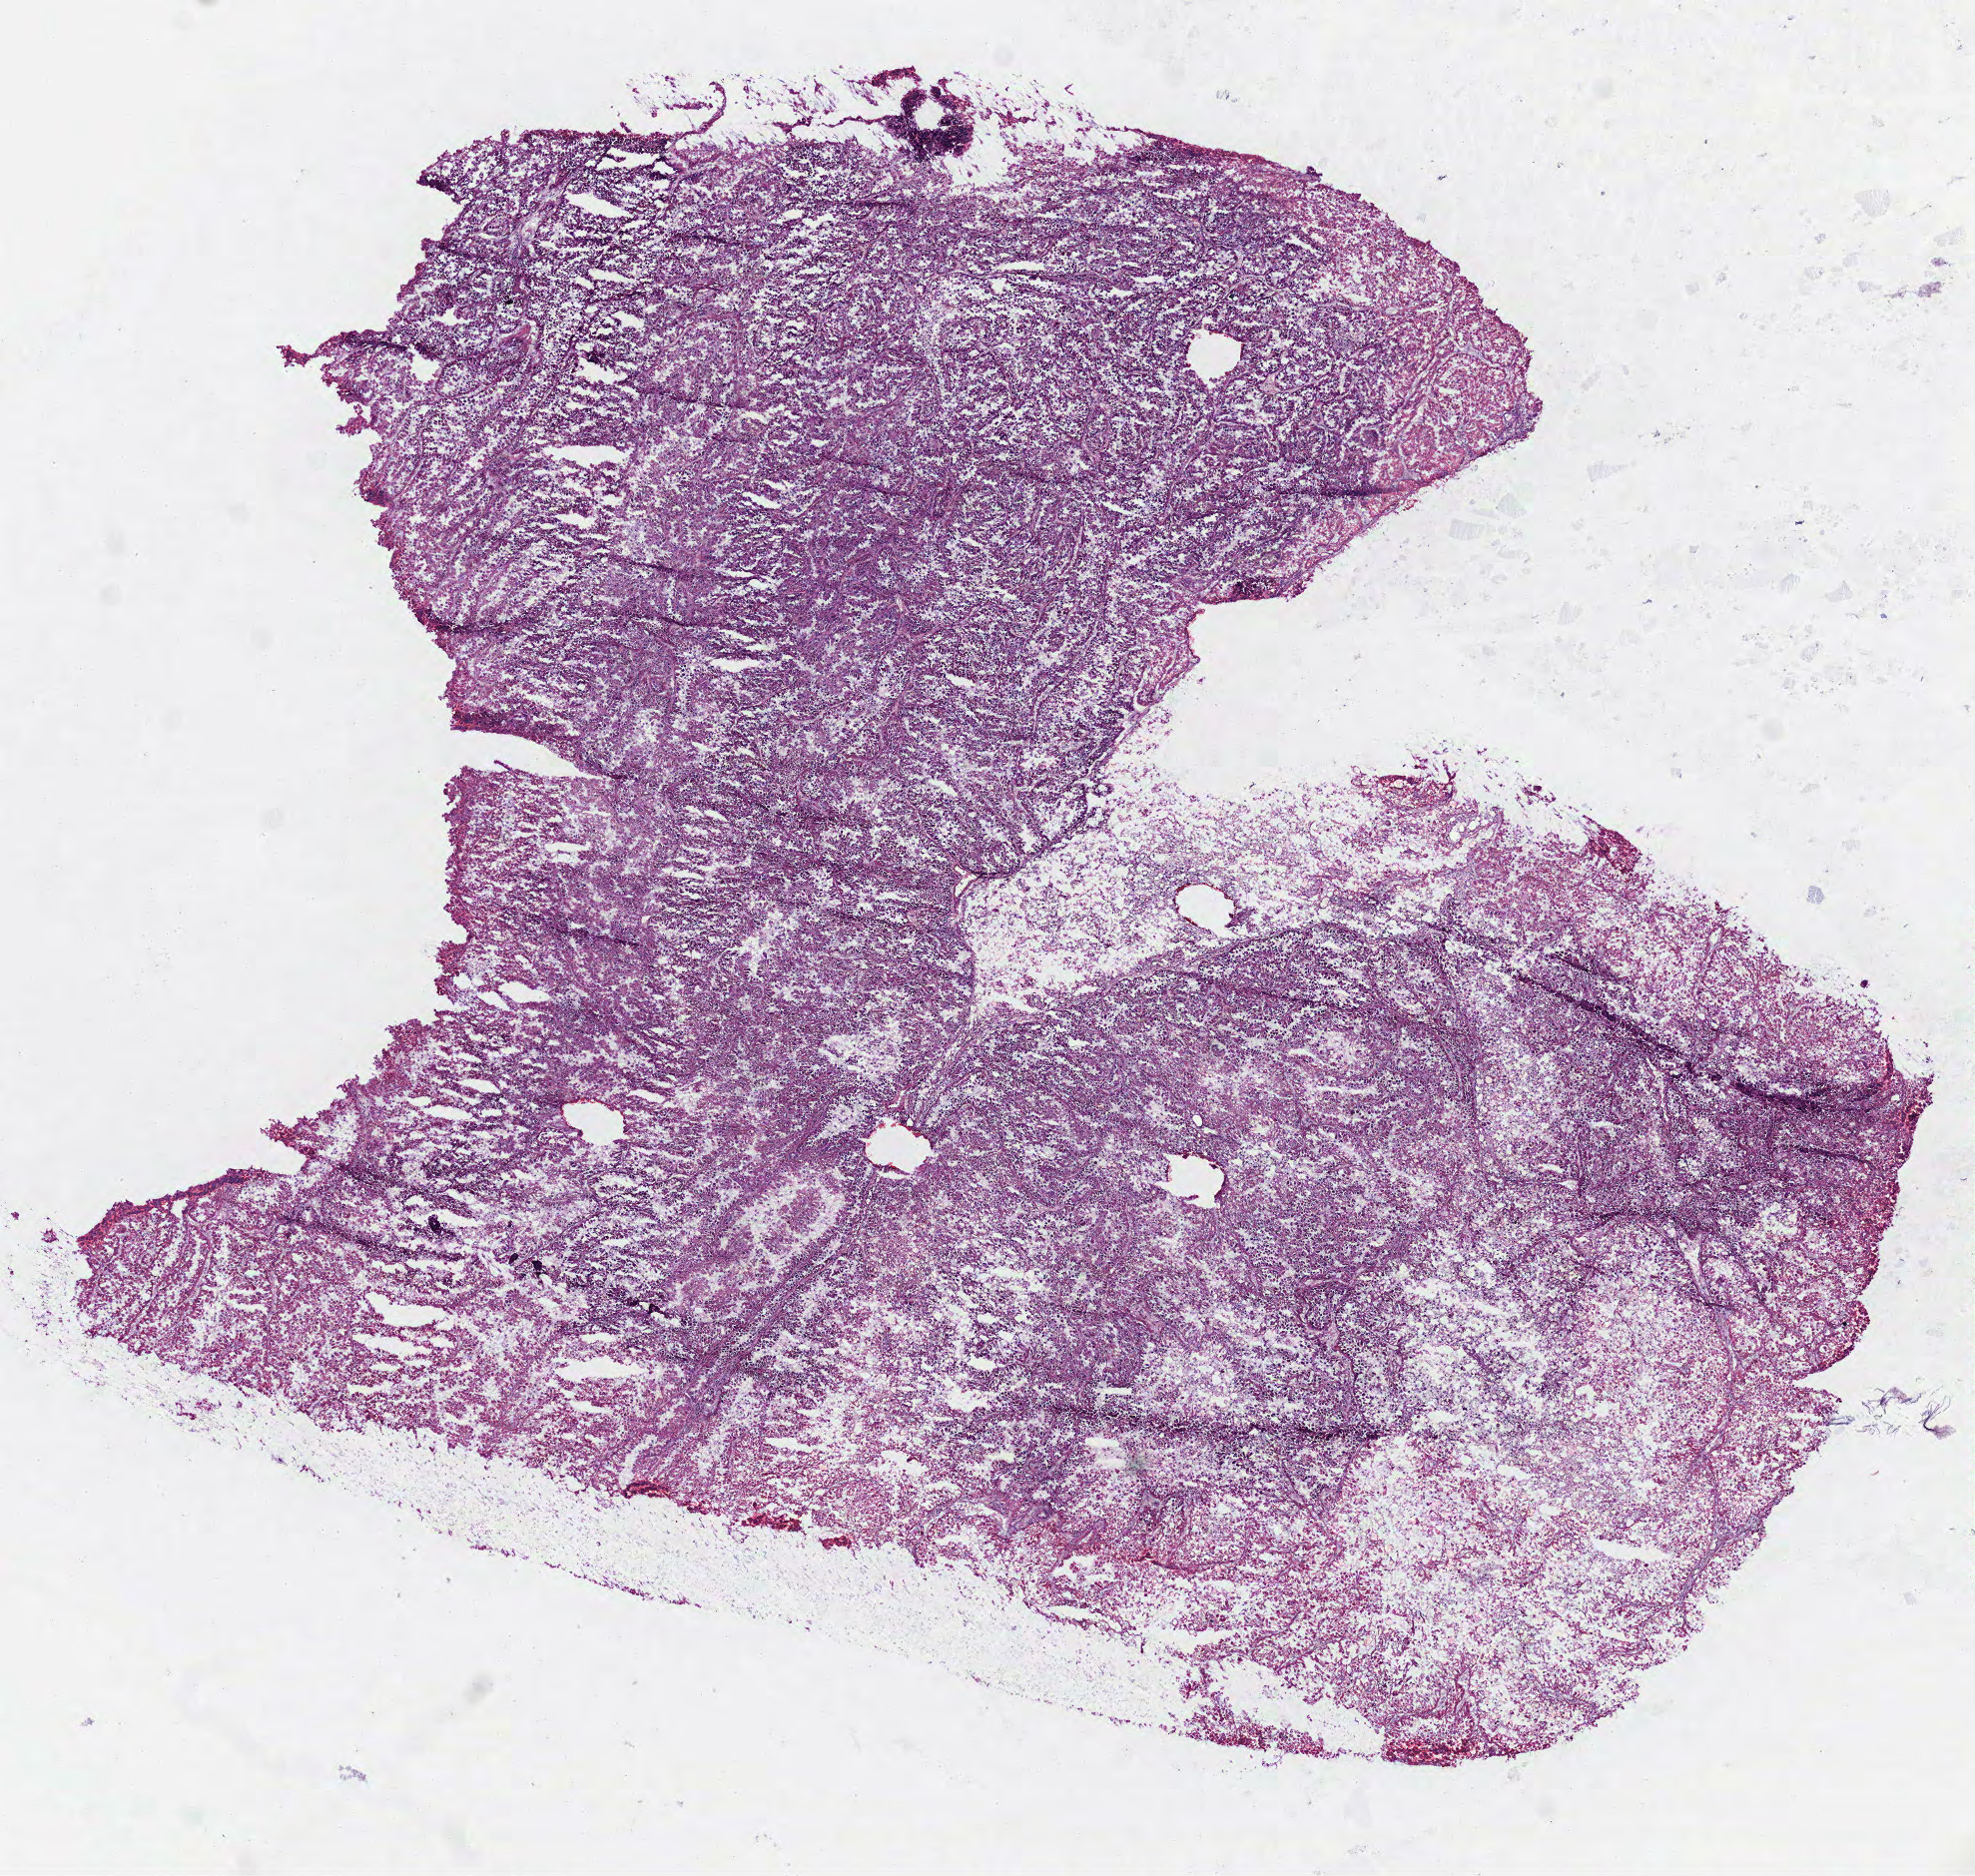
Whole-slide histology image, H&E, low-resolution overview of the scanned area, about 8.0 x 7.6 mm (acquisition: 40x scan). Frozen section from the top of the tissue portion. Sample: primary tumour, kidney. Male patient; age at initial diagnosis 58 years. Pathologist review of this section (percent, as recorded): tumour cells 100%, tumour nuclei 90%, normal cells 0%, stromal cells 0%, necrosis 0%. Infiltration values recorded for this section: lymphocyte infiltration 2%.
Histologic diagnosis: Papillary adenocarcinoma, NOS. AJCC pathologic stage: III.